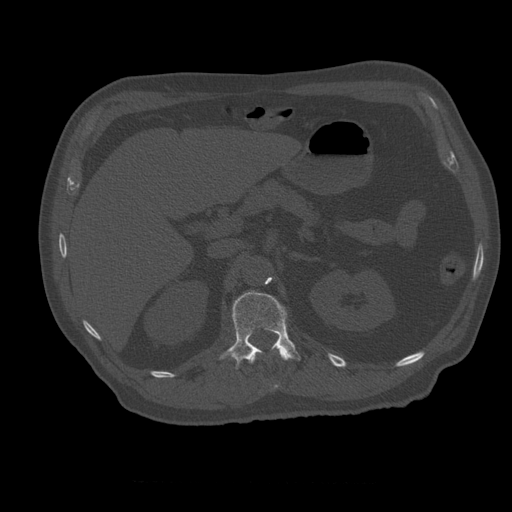
CT including the spine, one axial slice. Position 242 of 399 along the scan axis. Reconstruction kernel STANDARD. Bone window (W 1800 / L 400 HU). 512 × 512 image matrix, field of view 407 × 407 mm. Patient age 73 years. Case-level facts recorded for this patient, not image findings: primary cancer: prostate.
Annotated regions visible in this slice (semi-automatically segmented with operator editing):
- L1 vertebra: bounding box <220,291,301,369> (left, top, right, bottom; pixels)
- T12 vertebra: <249,347,292,389>